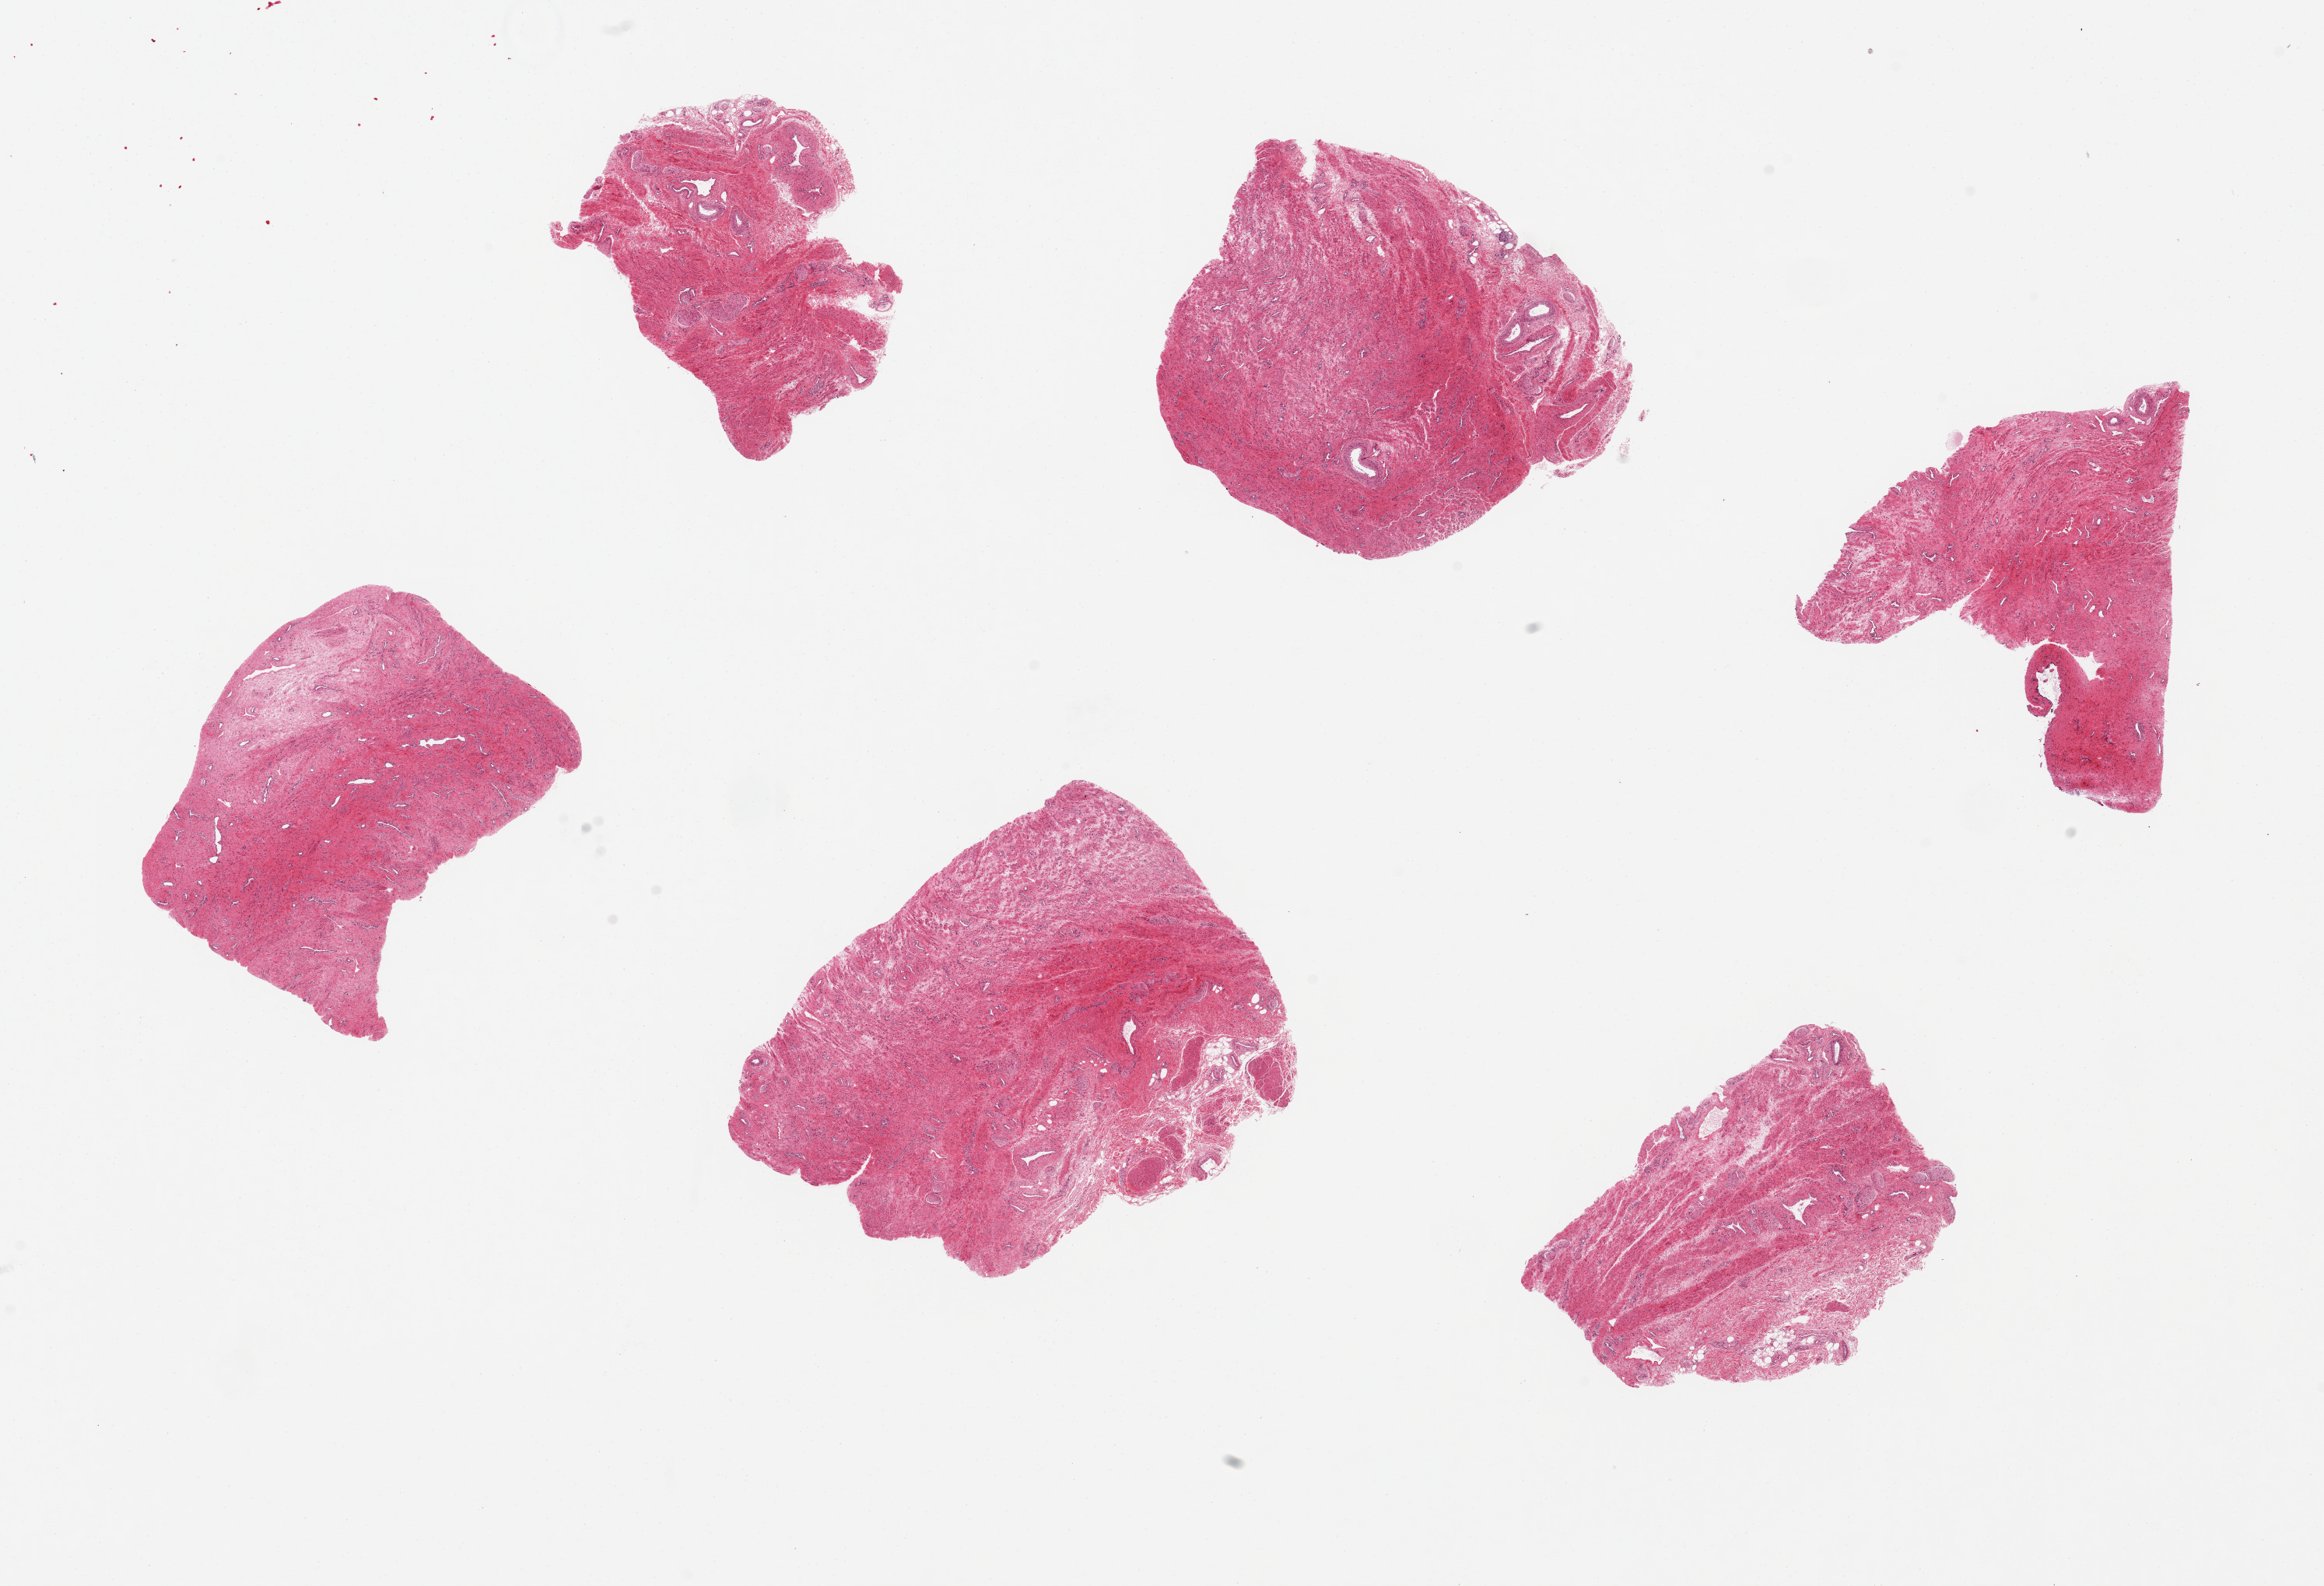
H&E whole-slide image, shown as a low-resolution overview of the whole scanned area (about 23.6 x 16.1 mm, from a 20x scan). PAXgene-fixed, paraffin-embedded tissue. Section of vagina (target tissue). Donor tissue sample. Donor: female.
Reviewer comment on this tissue sample: 6 pieces, up to 5x4mm; mucosa is sloughed on all pieces.